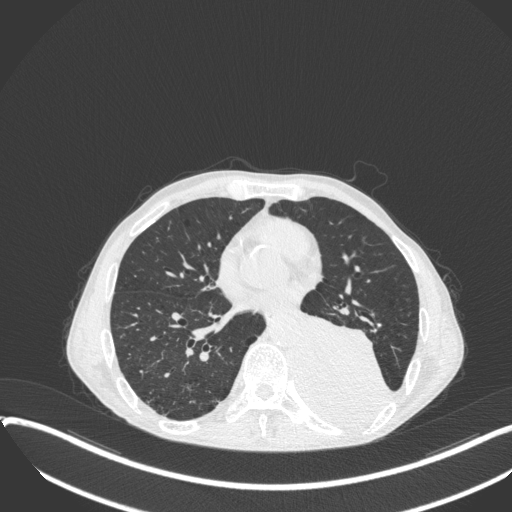
Chest CT, one axial slice. Position 156 of 400 along the scan axis. Reconstruction kernel B31f. 120 kVp. Lung window (W 1500 / L -600 HU). 512 × 512 image matrix, field of view 400 × 400 mm. Male patient, age 57 years. Case-level facts recorded for this patient, not image findings: clinical TNM (as recorded): T4 N0 M0.
Outlined on this slice (bounding box drawn by a radiologist):
- lung tumour (recorded histology: squamous cell carcinoma): bounding box [x1, y1, x2, y2] px = [293, 308, 393, 435]